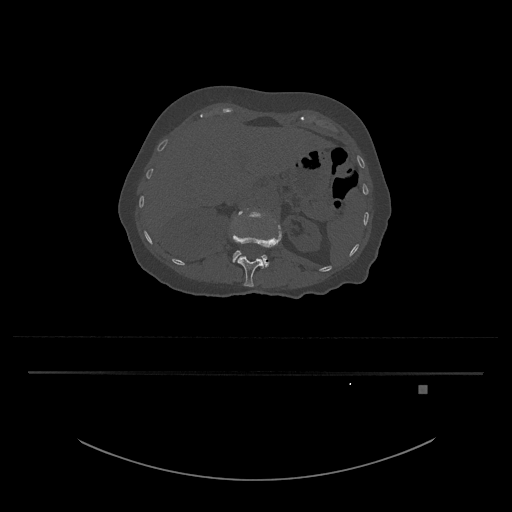
CT including the spine, one axial slice; position 534 of 797 along the scan axis; reconstruction kernel Br40s/3; 120 kVp; bone window (W 1800 / L 400 HU); 512 × 512 image matrix, field of view 500 × 500 mm. Female patient, age 57 years. From the clinical record (not read from this slice): primary cancer: cervical.
Outlined on this slice (semi-automatic segmentation, software-assisted and operator-edited):
- L1 vertebra: bounding box (x1, y1, x2, y2) in pixels: (232, 222, 282, 287)